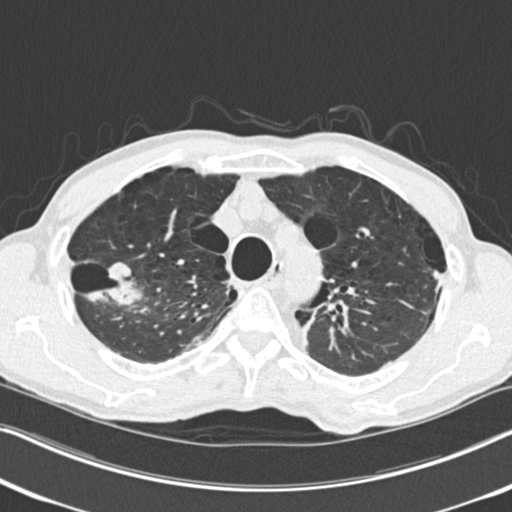
Low-dose screening chest CT, one axial slice. Slice 194 of 251 in the series (ordered by position). Reconstruction kernel B30f. 120 kVp. Lung window (W 1500 / L -600 HU). 2 mm slice thickness. 512 × 512 image matrix.
Outlined on this slice (manually delineated by an expert):
- lesion 1 (tumor, upper lobe of right lung): bounding box <87,262,140,307> (left, top, right, bottom; pixels)